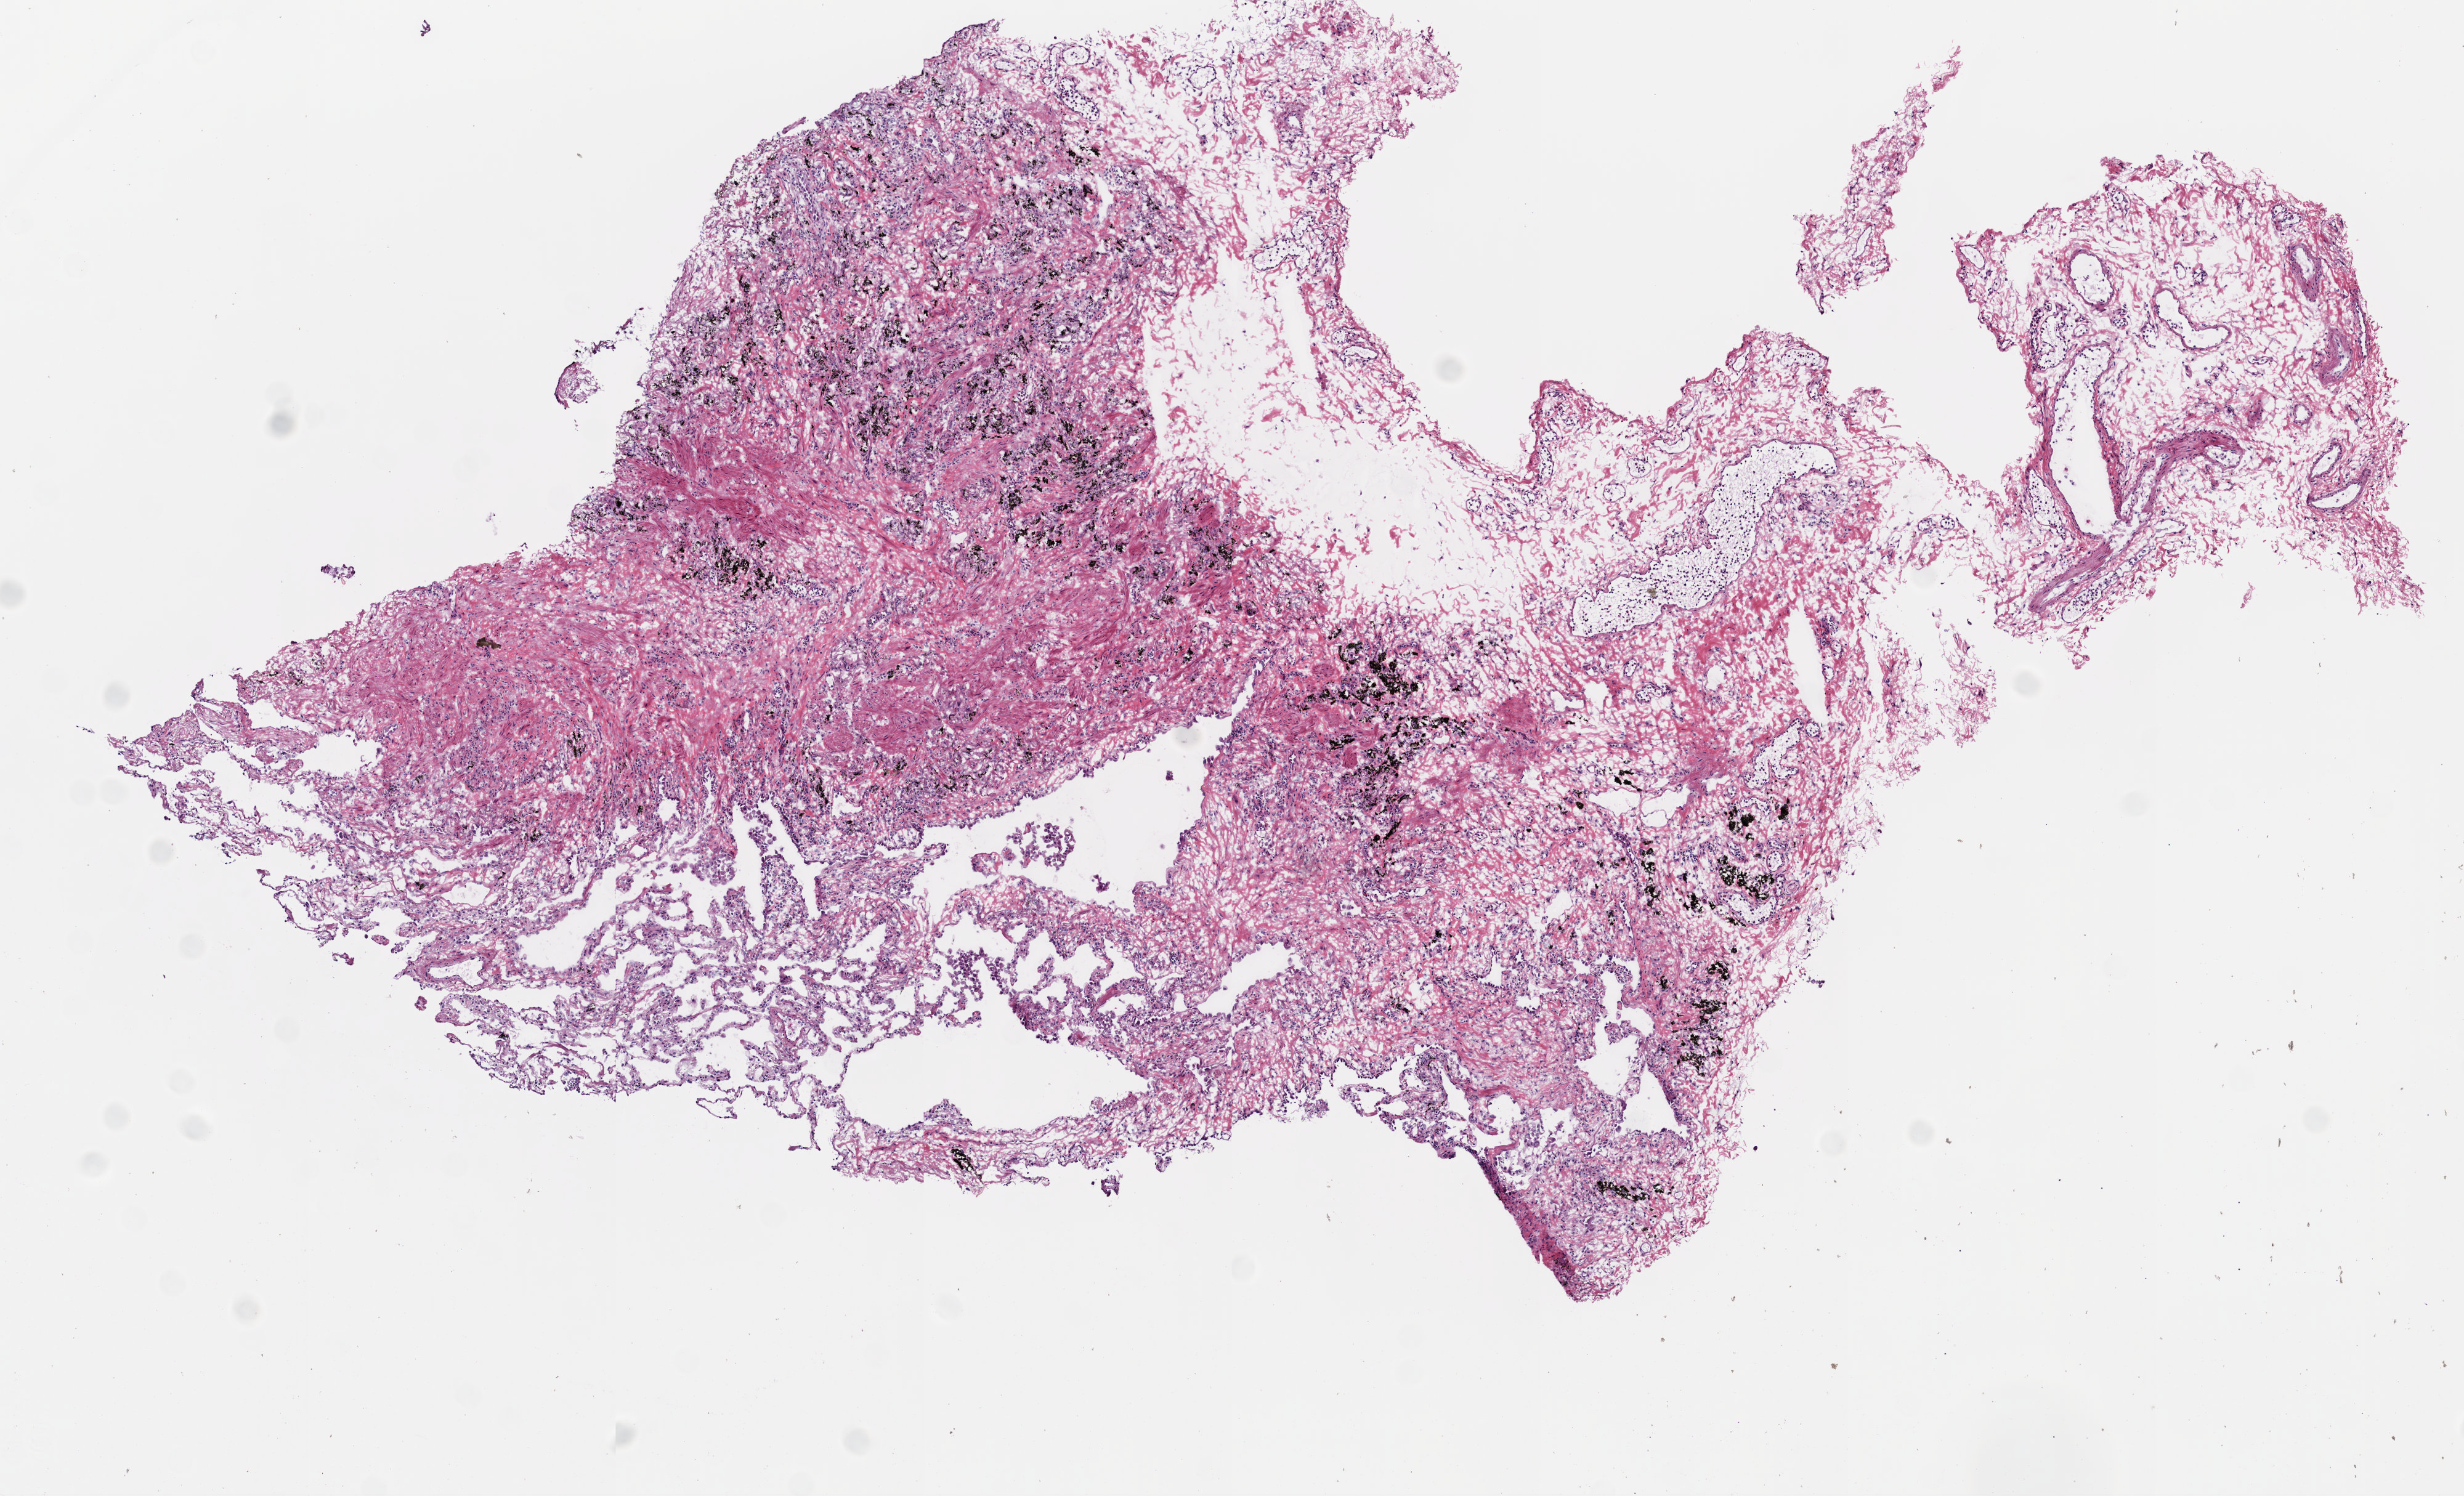
H&E-stained whole-slide image, a low-resolution overview of the entire scanned area, about 8.0 x 4.9 mm; frozen section from the bottom of the tissue portion; sample: solid tissue normal (non-tumour tissue), lung. Male patient; age at initial diagnosis 75 years.
This section: solid tissue normal (non-tumour) sample from the same patient. Patient diagnosis: Squamous cell carcinoma, NOS (lower lobe, lung).